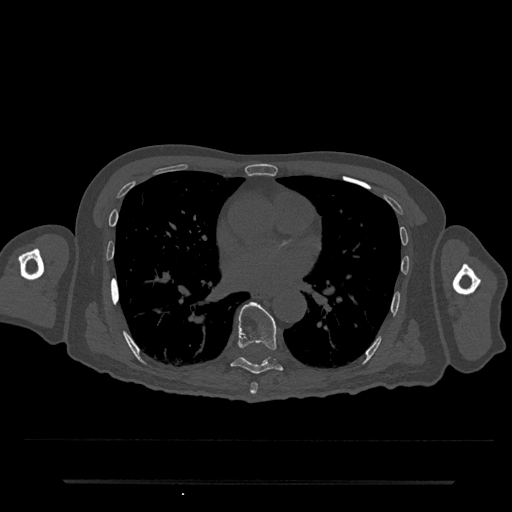
CT including the spine, one axial slice. Slice 423 of 797 in the series (ordered by position). Reconstruction kernel Br40s/3. Bone window (W 1800 / L 400 HU). 0.5 mm slice thickness. 512 × 512 image matrix. Patient: male, 74 years. From the clinical record (not read from this slice): primary cancer: prostate.
Outlined on this slice (semi-automatic segmentation, software-assisted and operator-edited):
- T7 vertebra: bounding box <250,382,258,395> (left, top, right, bottom; pixels)
- T8 vertebra: <231,302,283,374>